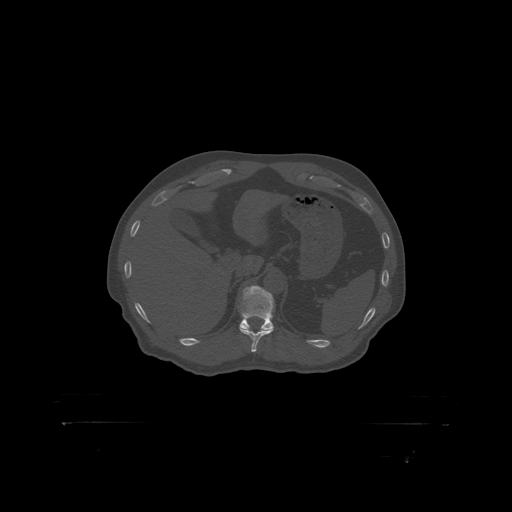
CT including the spine, one axial slice; slice 367 of 399 in the series (ordered by position); reconstruction kernel STANDARD; bone window (W 1800 / L 400 HU); 512 × 512 image matrix. Patient: male, 46 years. From the clinical record (not read from this slice): primary cancer: skin.
Outlined on this slice (semi-automatically segmented with operator editing):
- T12 vertebra: bounding box (x1, y1, x2, y2) in pixels: (240, 287, 275, 319)